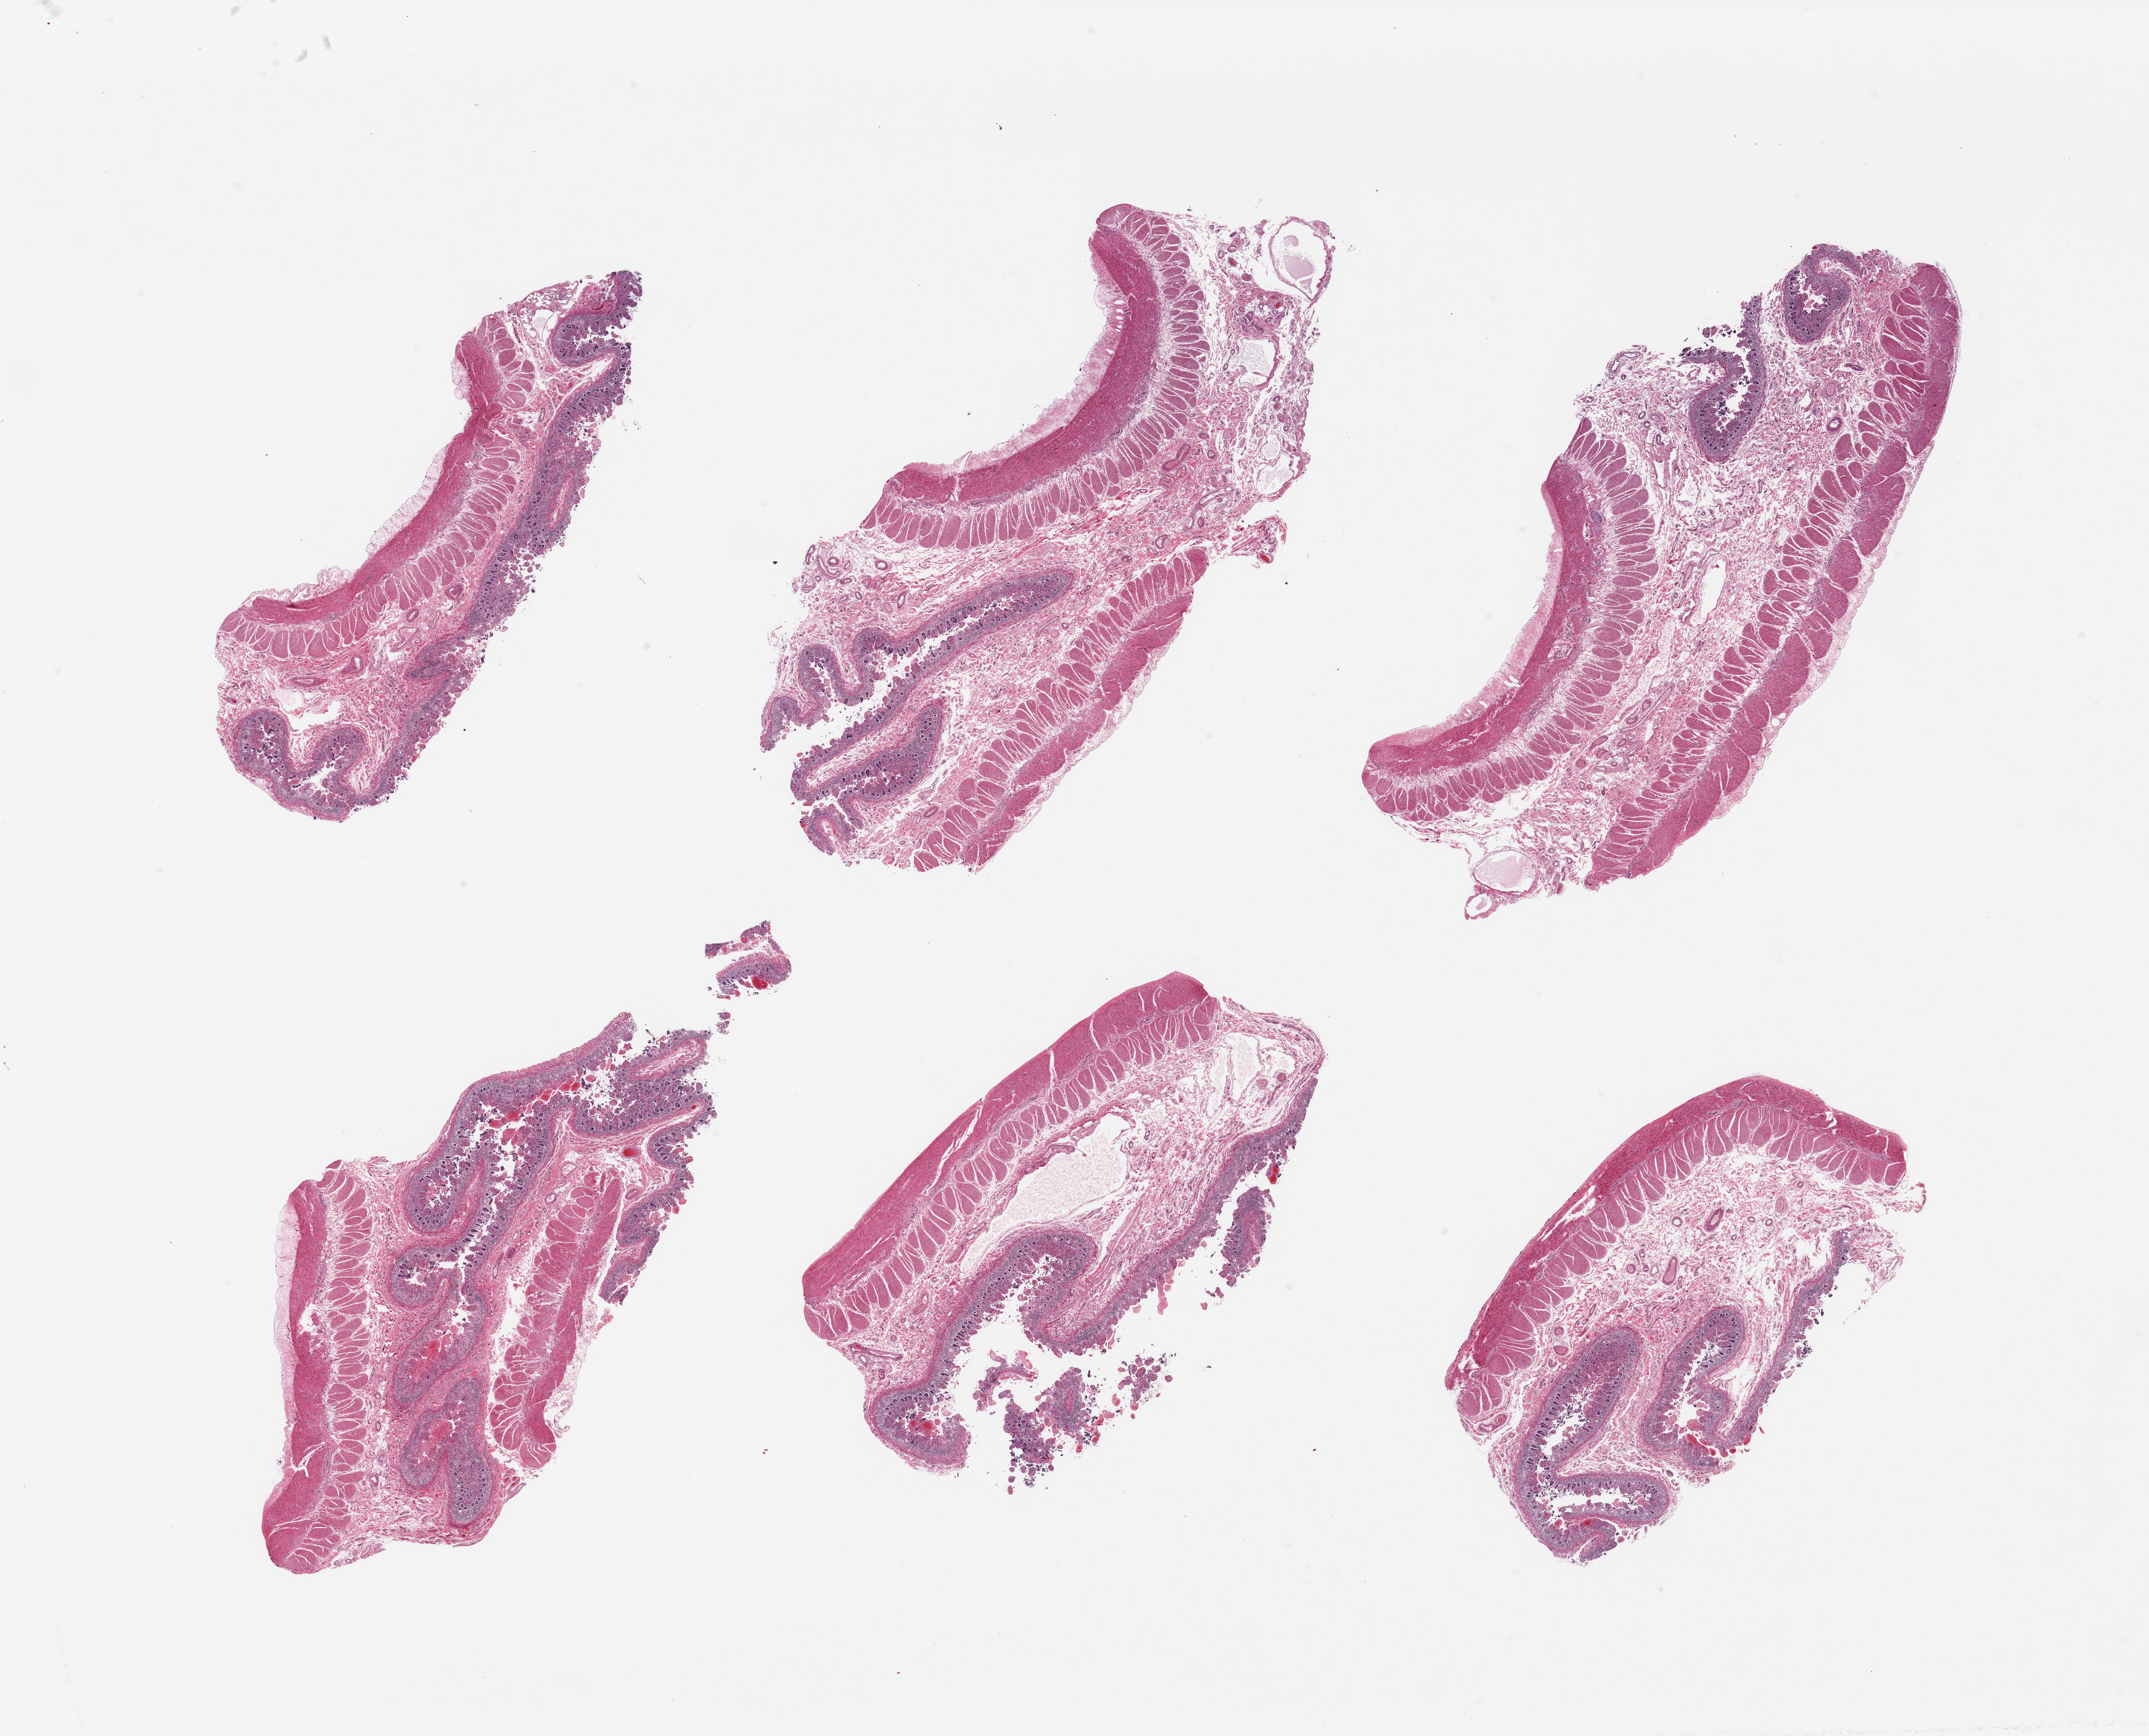
Hematoxylin and eosin (H&E) whole-slide image, a low-resolution overview of the entire scanned area, about 27.6 x 22.3 mm (slide scanned at 20x); PAXgene-fixed, paraffin-embedded tissue; section of transverse colon (target tissue); tissue donor sample. Donor sex: male.
• pathologist's review note for this sample: 6 pieces; mucosa severely autolyzed; muscularis moderately autolyzed